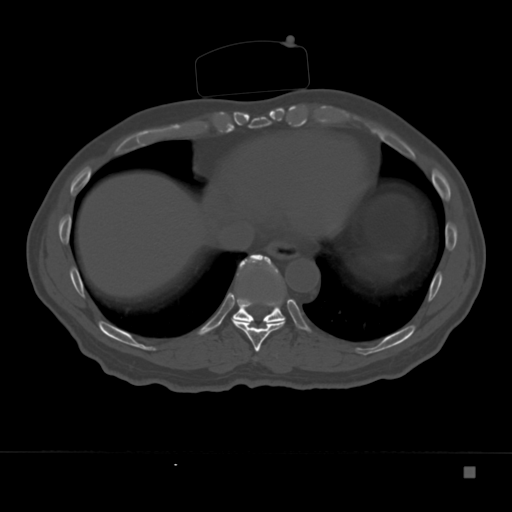
CT including the spine, one axial slice. Position 182 of 332 along the scan axis. Bone window (W 1800 / L 400 HU). 1.5 mm slice thickness. 512 × 512 image matrix, field of view 389 × 389 mm. Male patient, age 72 years. Case-level facts recorded for this patient, not image findings: primary cancer: skeletal.
Outlined on this slice (semi-automatically segmented with operator editing):
- T10 vertebra: bounding box [x1, y1, x2, y2] px = [232, 255, 285, 323]
- T9 vertebra: [232, 254, 285, 352]